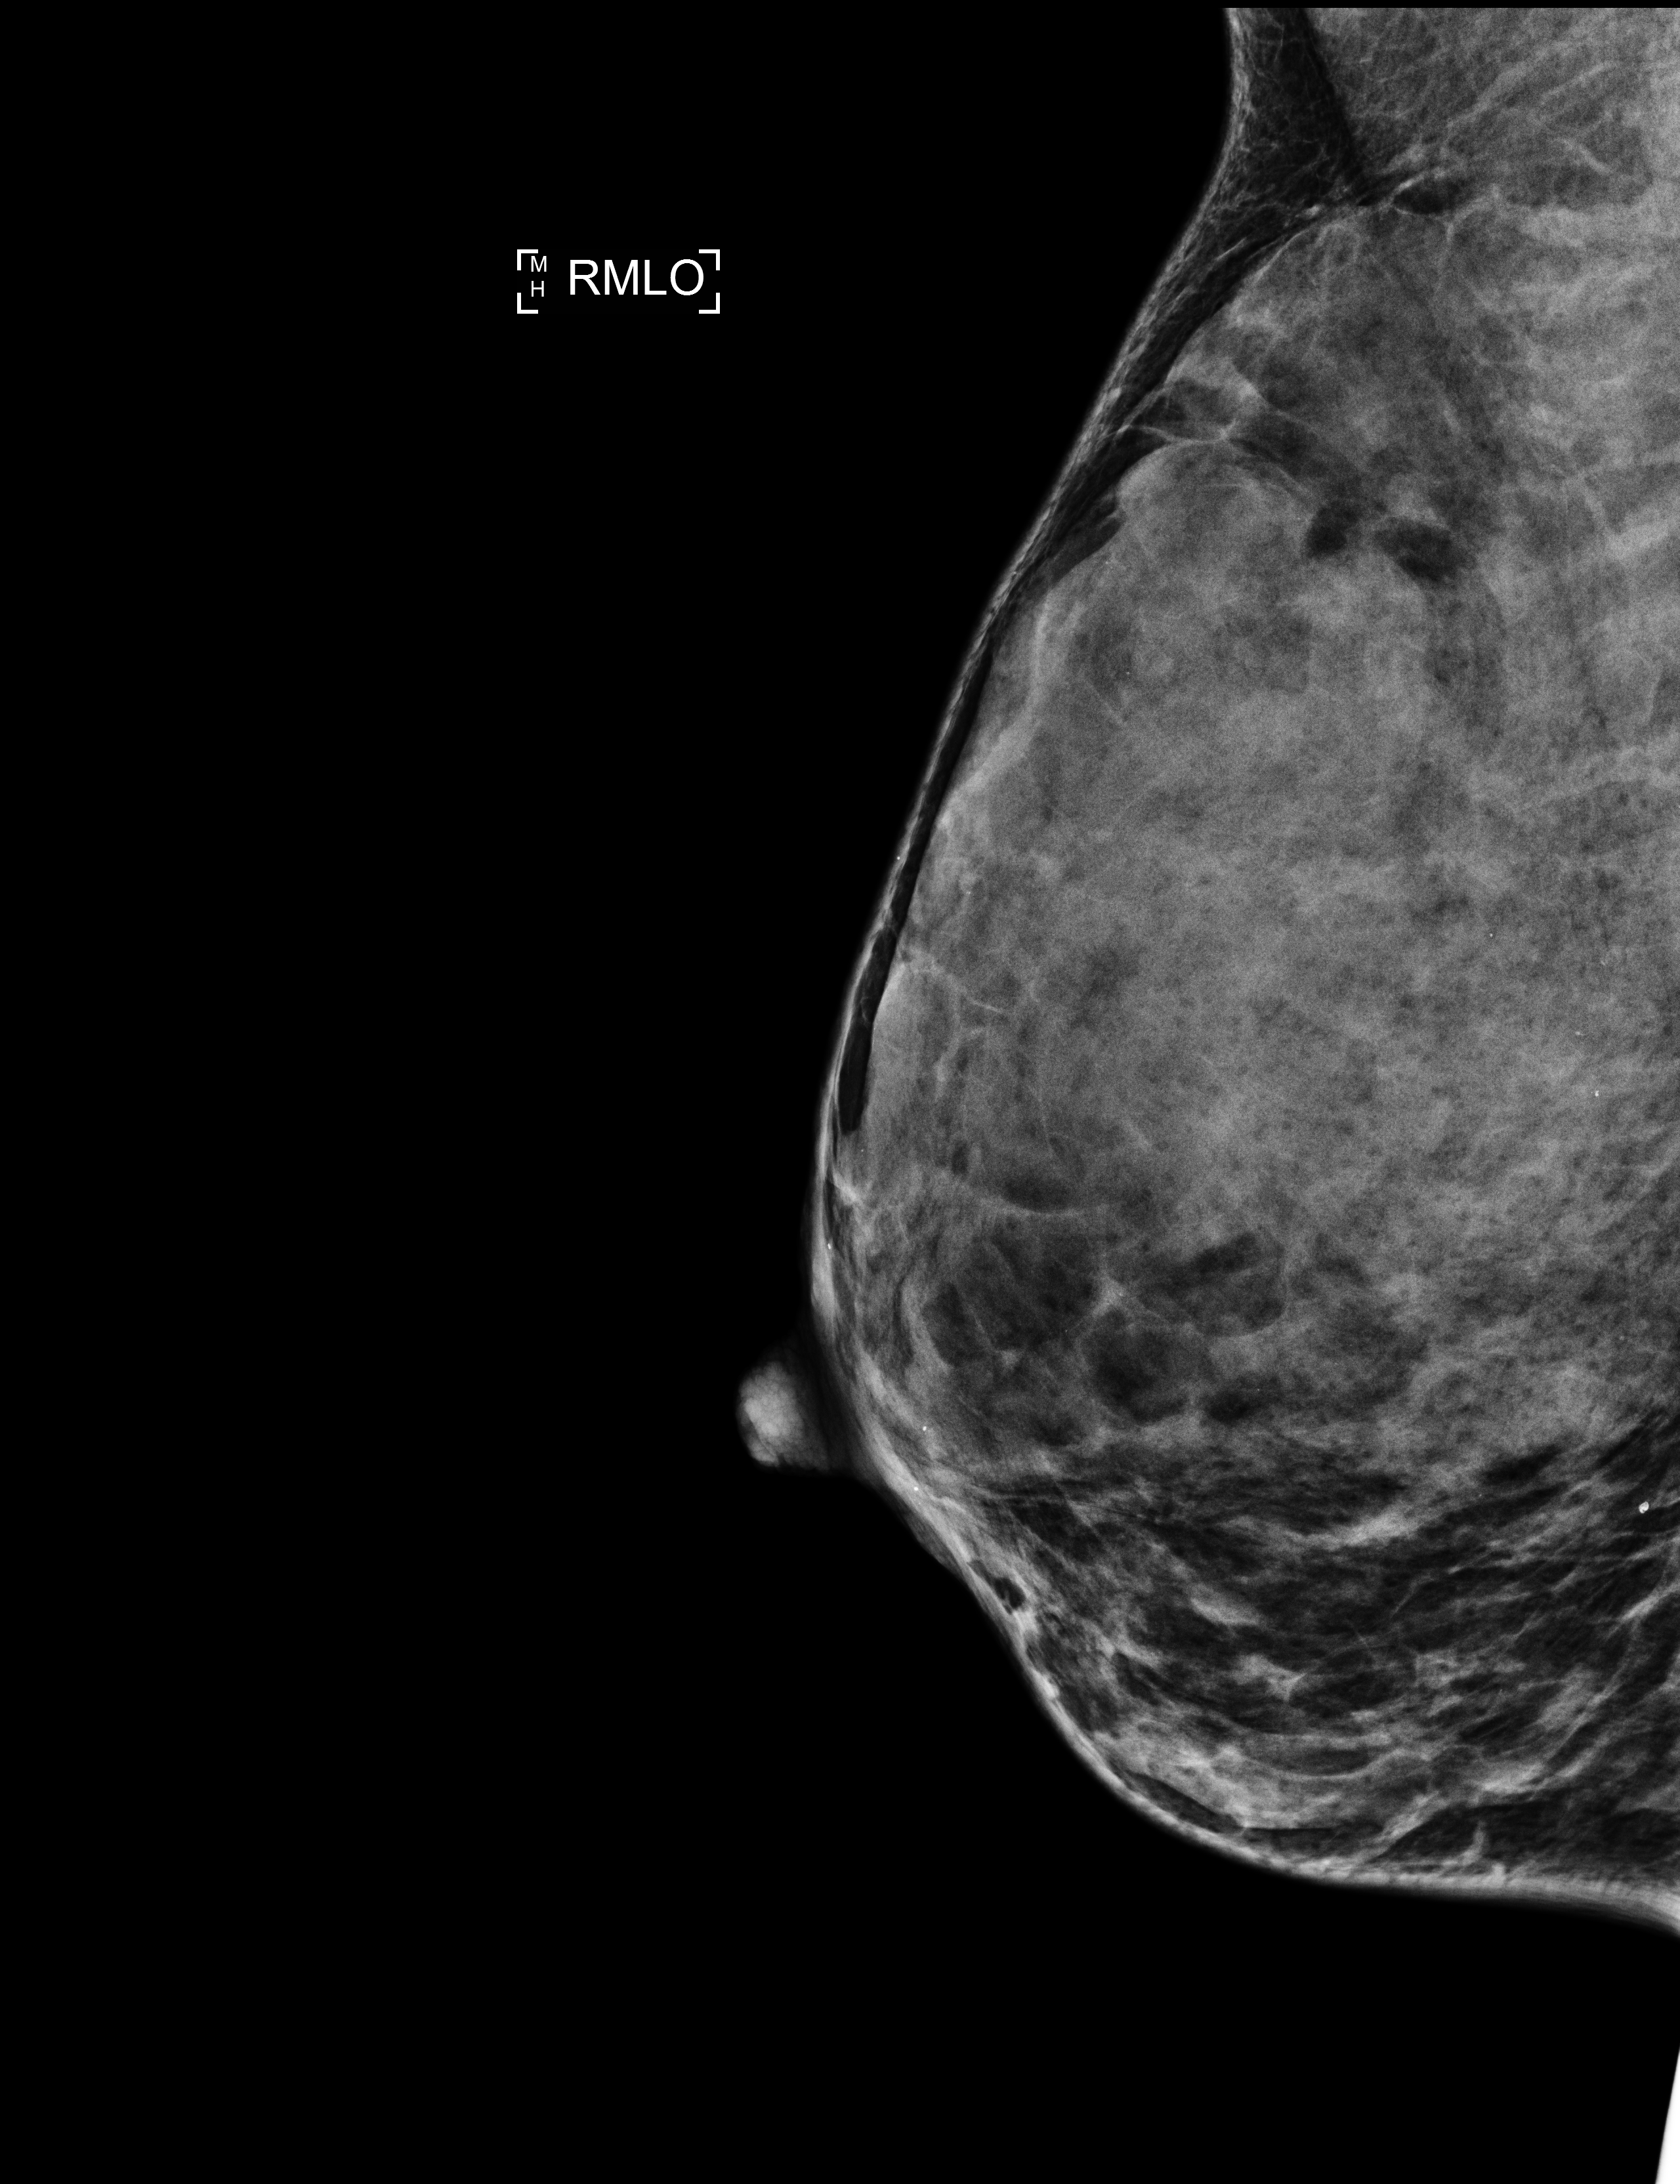
Annual screening mammography examination, compressed breast thickness 38 mm, system: Selenia Dimensions. Patient: female, 42 years.
Image type: full-field digital mammogram. Breast: right. Projection: medio-lateral oblique projection.